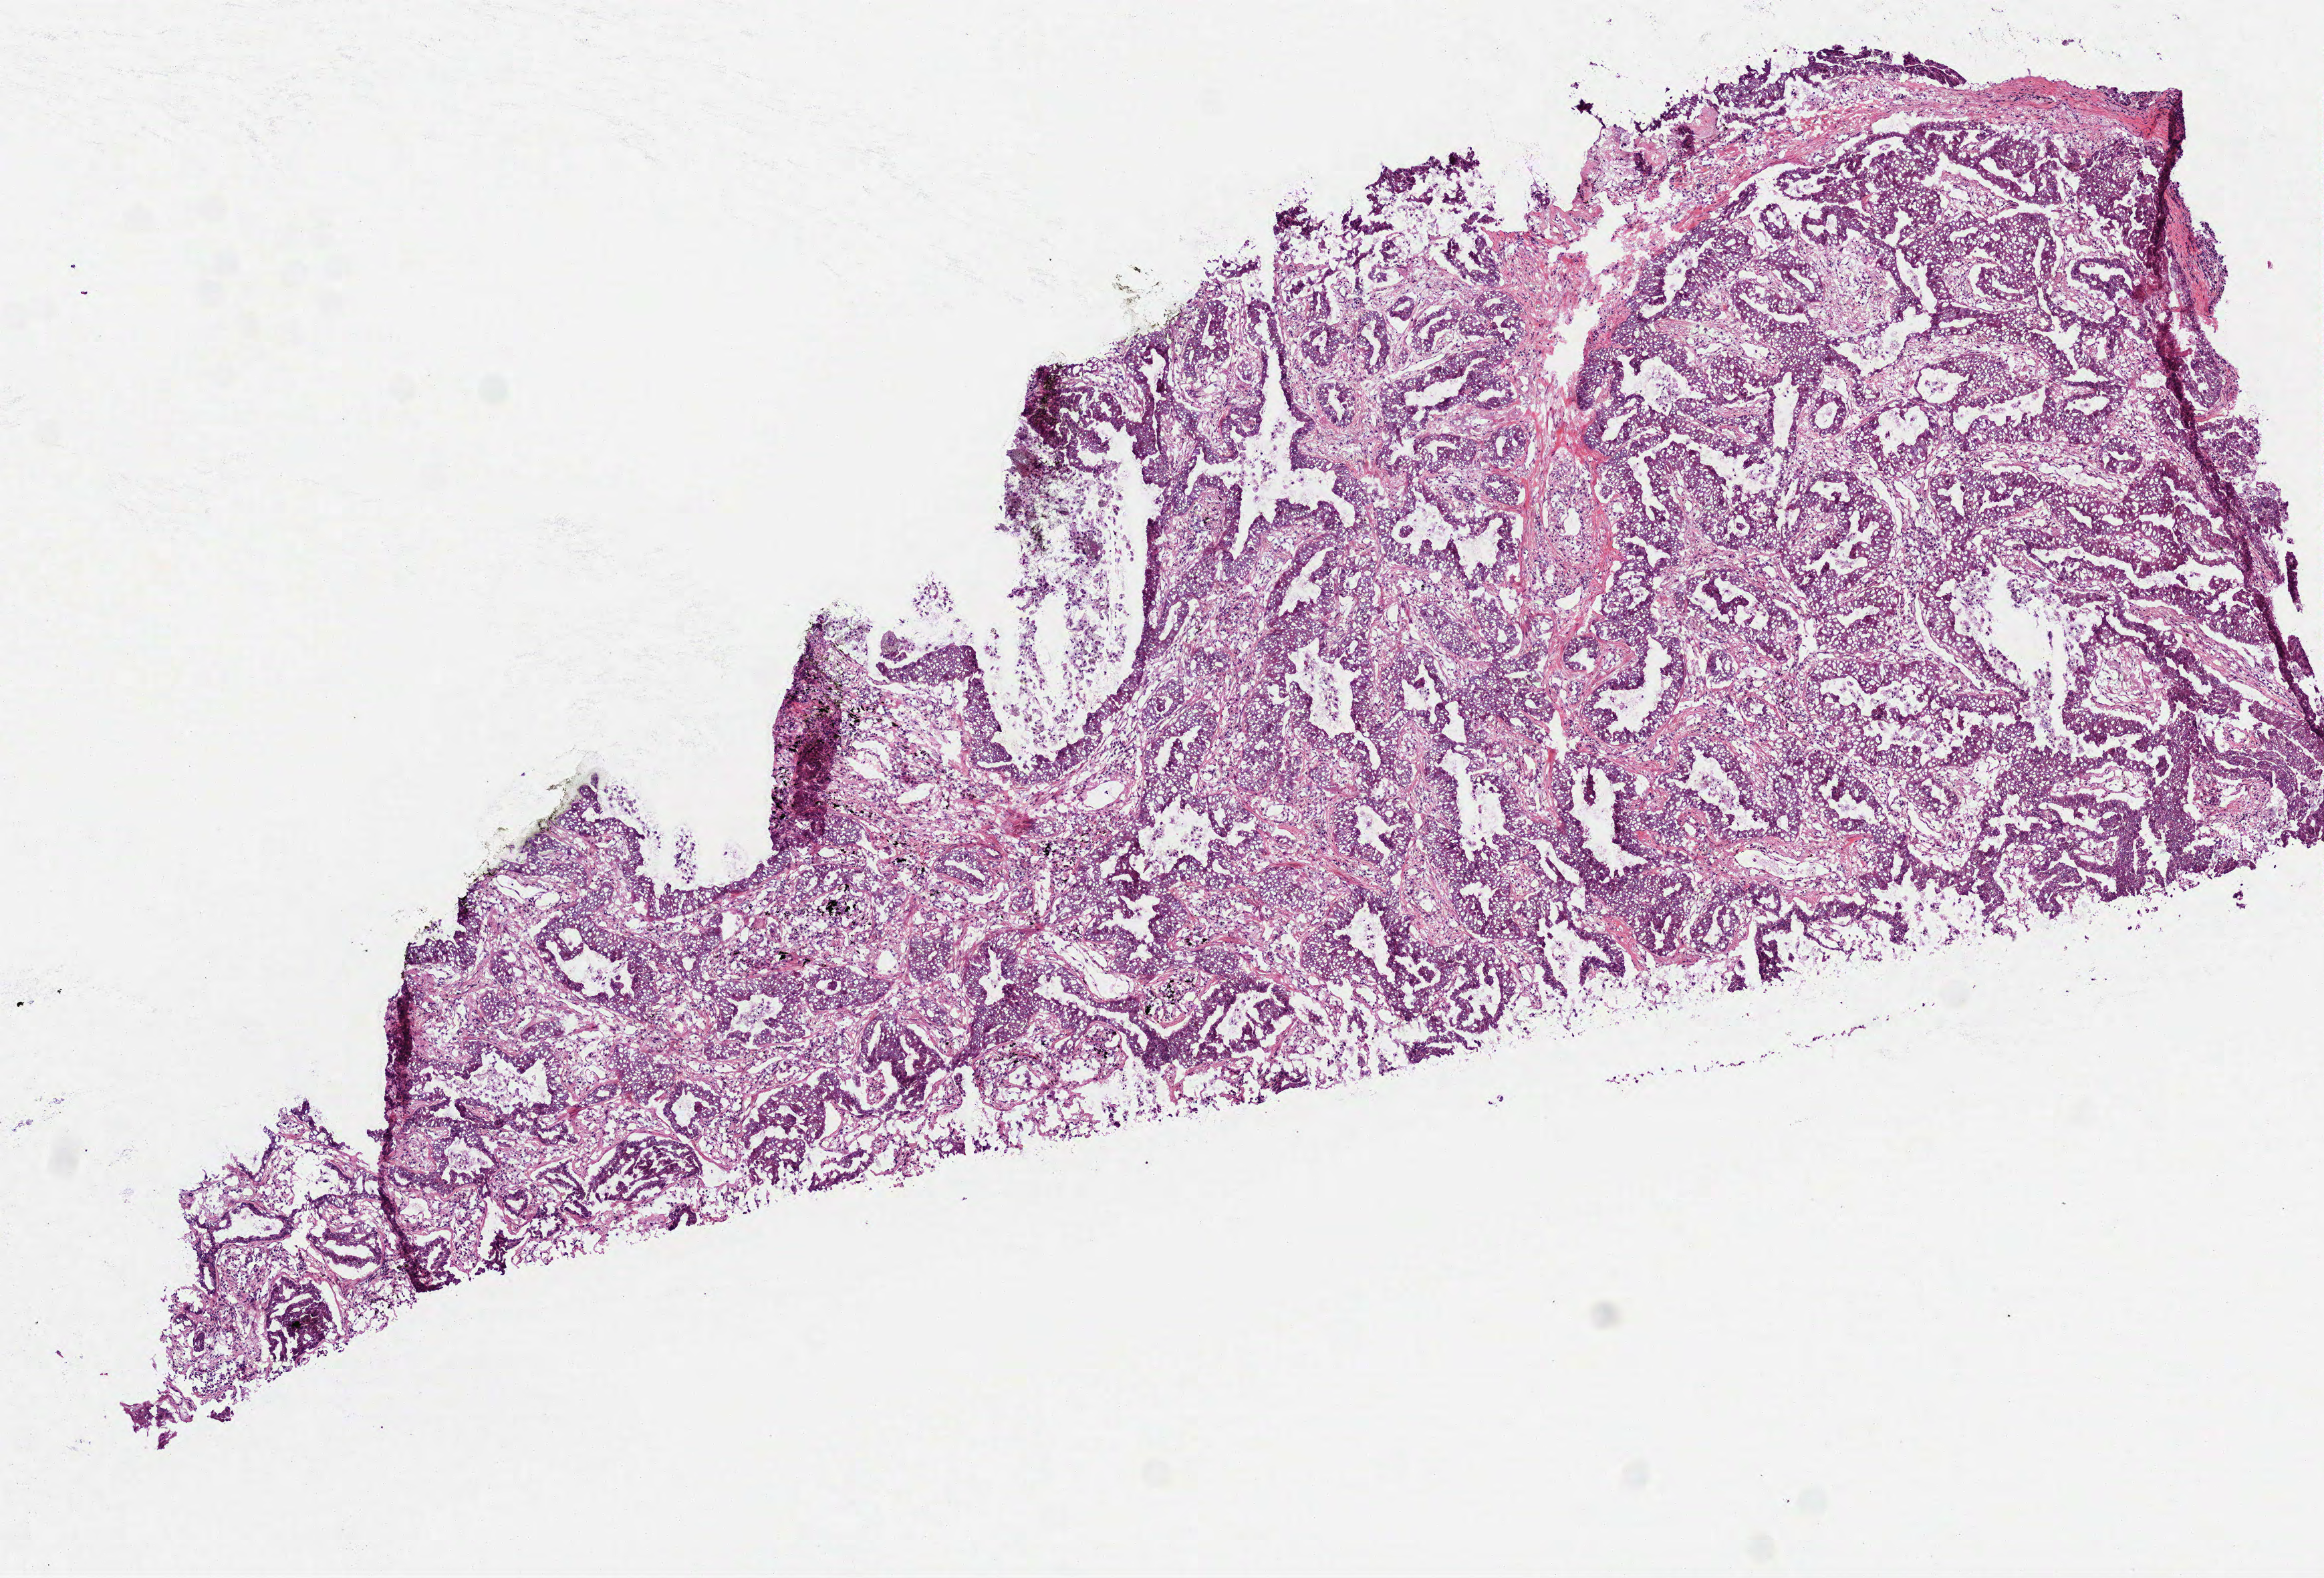
Digitized H&E tissue section (whole slide) — low-resolution overview of the scanned area, about 7.0 x 4.8 mm; frozen section from the top of the tissue portion; lung, primary tumour sample. Patient: female, age at initial diagnosis 65 years. Pathologist review of this section (percent, as recorded): tumour cells 90%, tumour nuclei 75%, normal cells 0%, stromal cells 10%, necrosis 0%.
- AJCC pathologic stage: IB
- pathologic diagnosis: Adenocarcinoma with mixed subtypes
- laterality: right